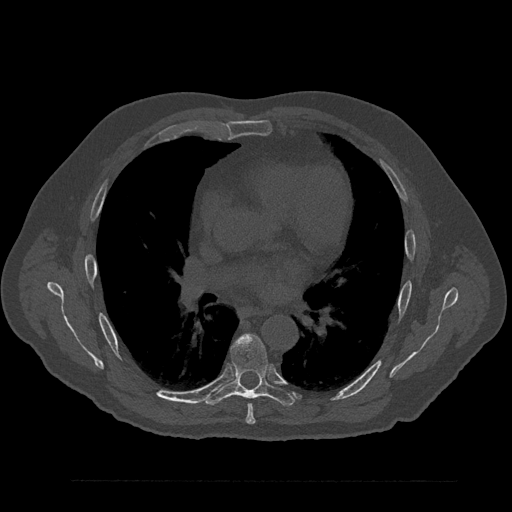
CT including the spine, one axial slice. 120 kVp. Bone window (W 1800 / L 400 HU). 0.5 mm slice thickness. 512 × 512 image matrix. Male patient, age 61 years. Case-level facts recorded for this patient, not image findings: primary cancer: prostate.
Outlined on this slice (semi-automatically segmented with operator editing):
- T6 vertebra: bounding box (x1, y1, x2, y2) in pixels: (246, 403, 256, 424)
- T7 vertebra: (204, 334, 295, 406)